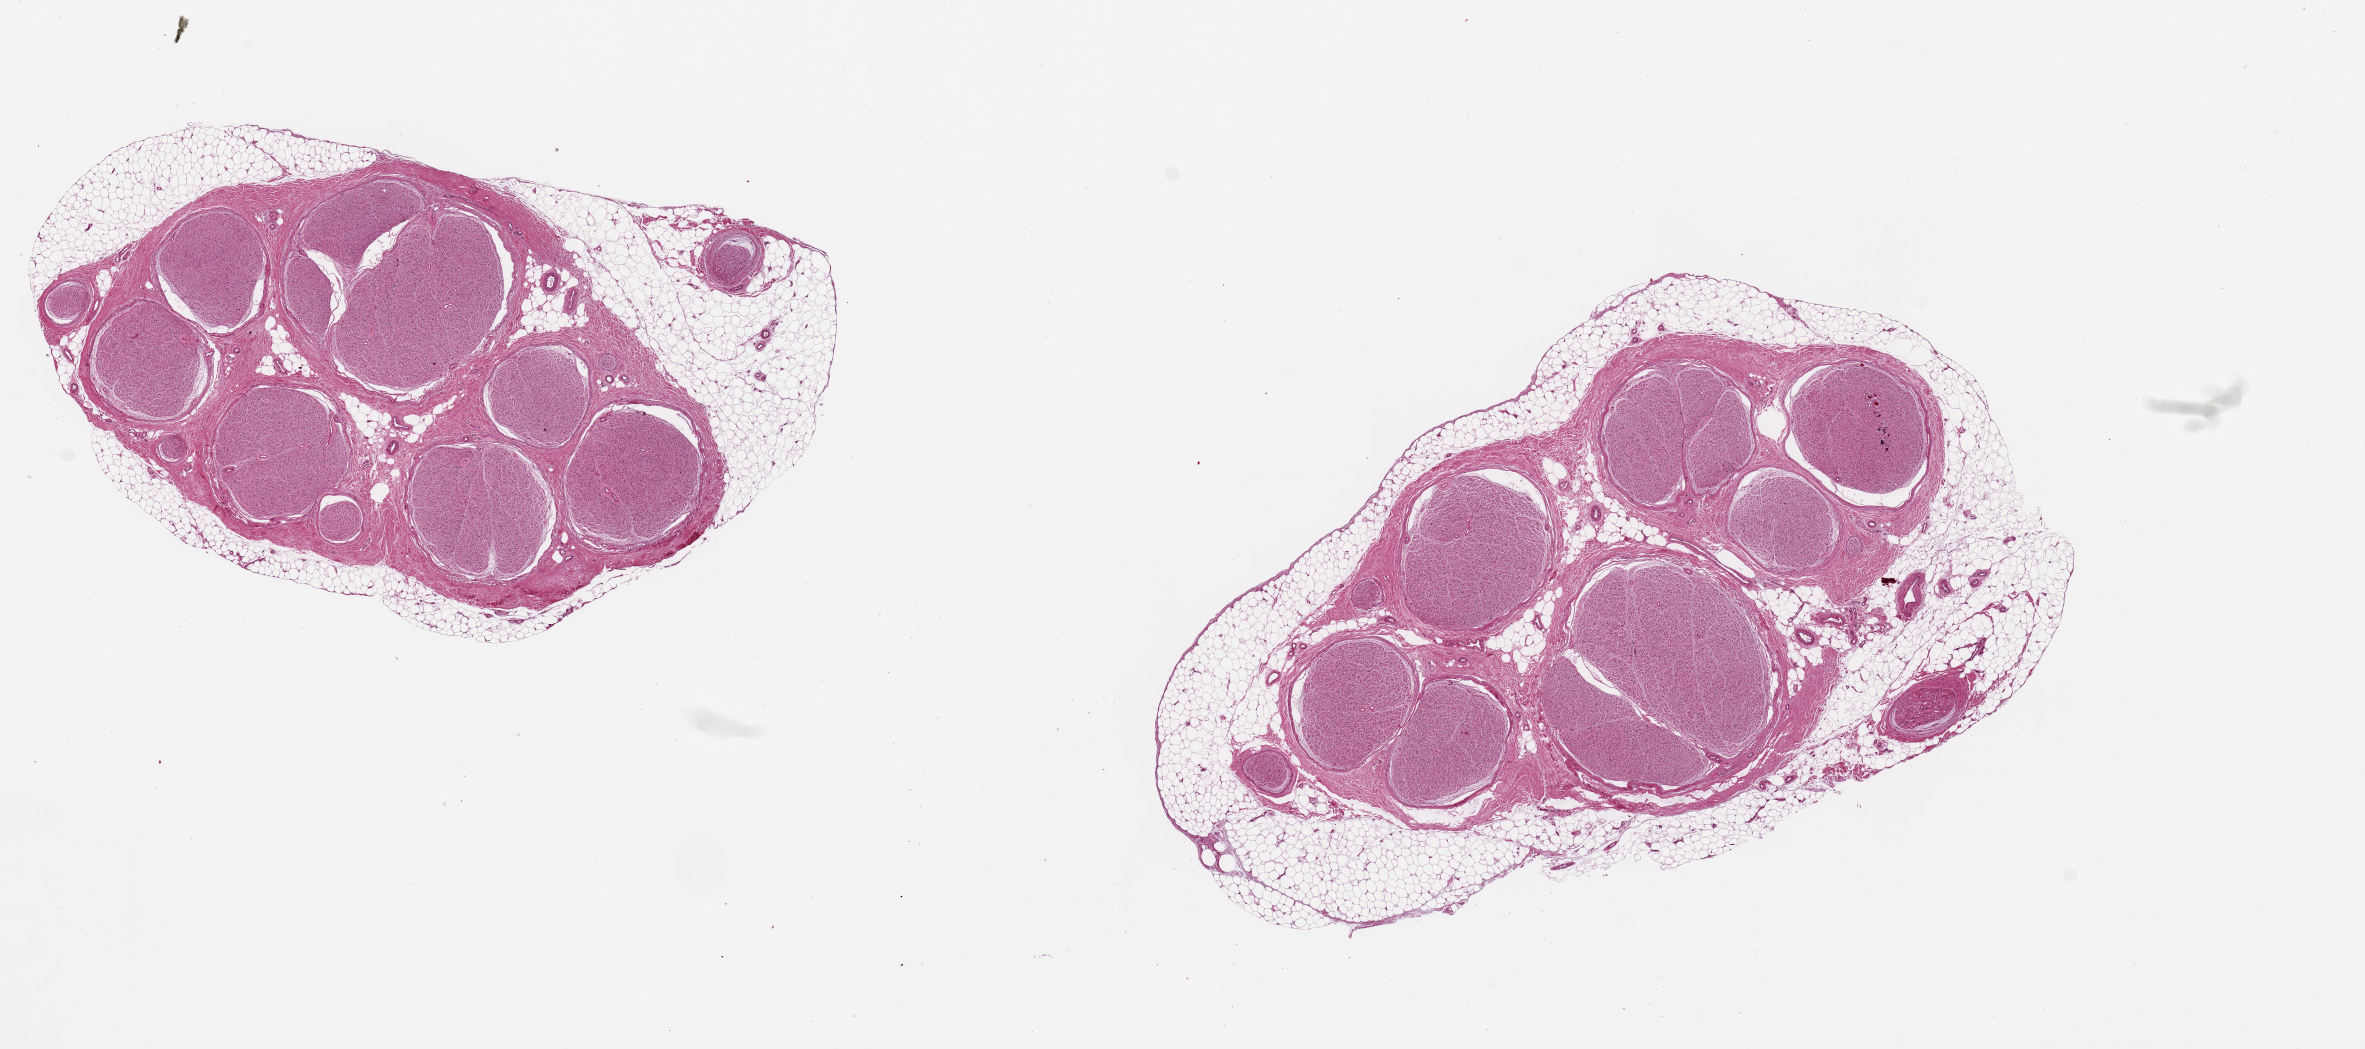
Digitized hematoxylin and eosin (H&E)-stained section — shown as a low-resolution overview of the whole scanned area (about 18.7 x 8.3 mm); PAXgene-fixed paraffin-embedded (PFPE) section; section of tibial nerve (target tissue); donor tissue sample. Male donor.
* review note (as recorded): 2 pieces ~4mm d; Nerve tissue in both, up to 1.5mm discontinuous rim of adherent fat on both